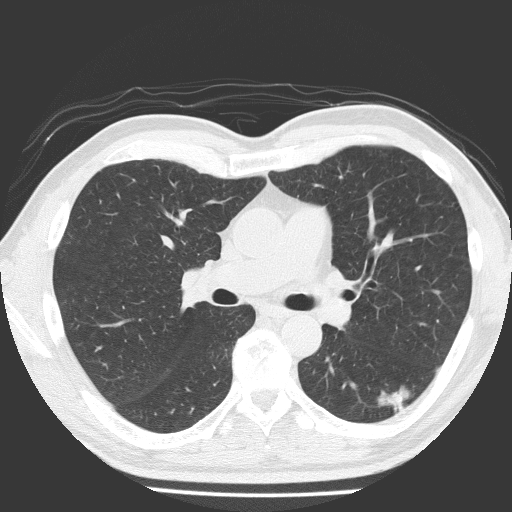
Low-dose screening chest CT, axial slice; baseline annual screen; lung window (W 1500 / L -600 HU); 2 mm slice thickness; lung (sharp) reconstruction kernel (FC51); 120 kVp; slice 77 of 184 in the series; 512 × 512 image matrix, field of view 348 × 348 mm. Male, age 58 years at enrolment. Current smoker at enrolment.
Expert-annotated lung lesion, bounding box (x1, y1, x2, y2) in pixels: (367, 374, 426, 423). The screening reader recorded 4 non-calcified nodules or masses ≥4 mm on this exam (left lower lobe, left lower lobe, right middle lobe, left upper lobe); which of them this box marks is not recorded. Lung cancer was diagnosed 99 days after this screen: adenosquamous carcinoma, left lower lobe, moderately differentiated (G2), stage IA (AJCC 6th edition), 28 mm at pathology.